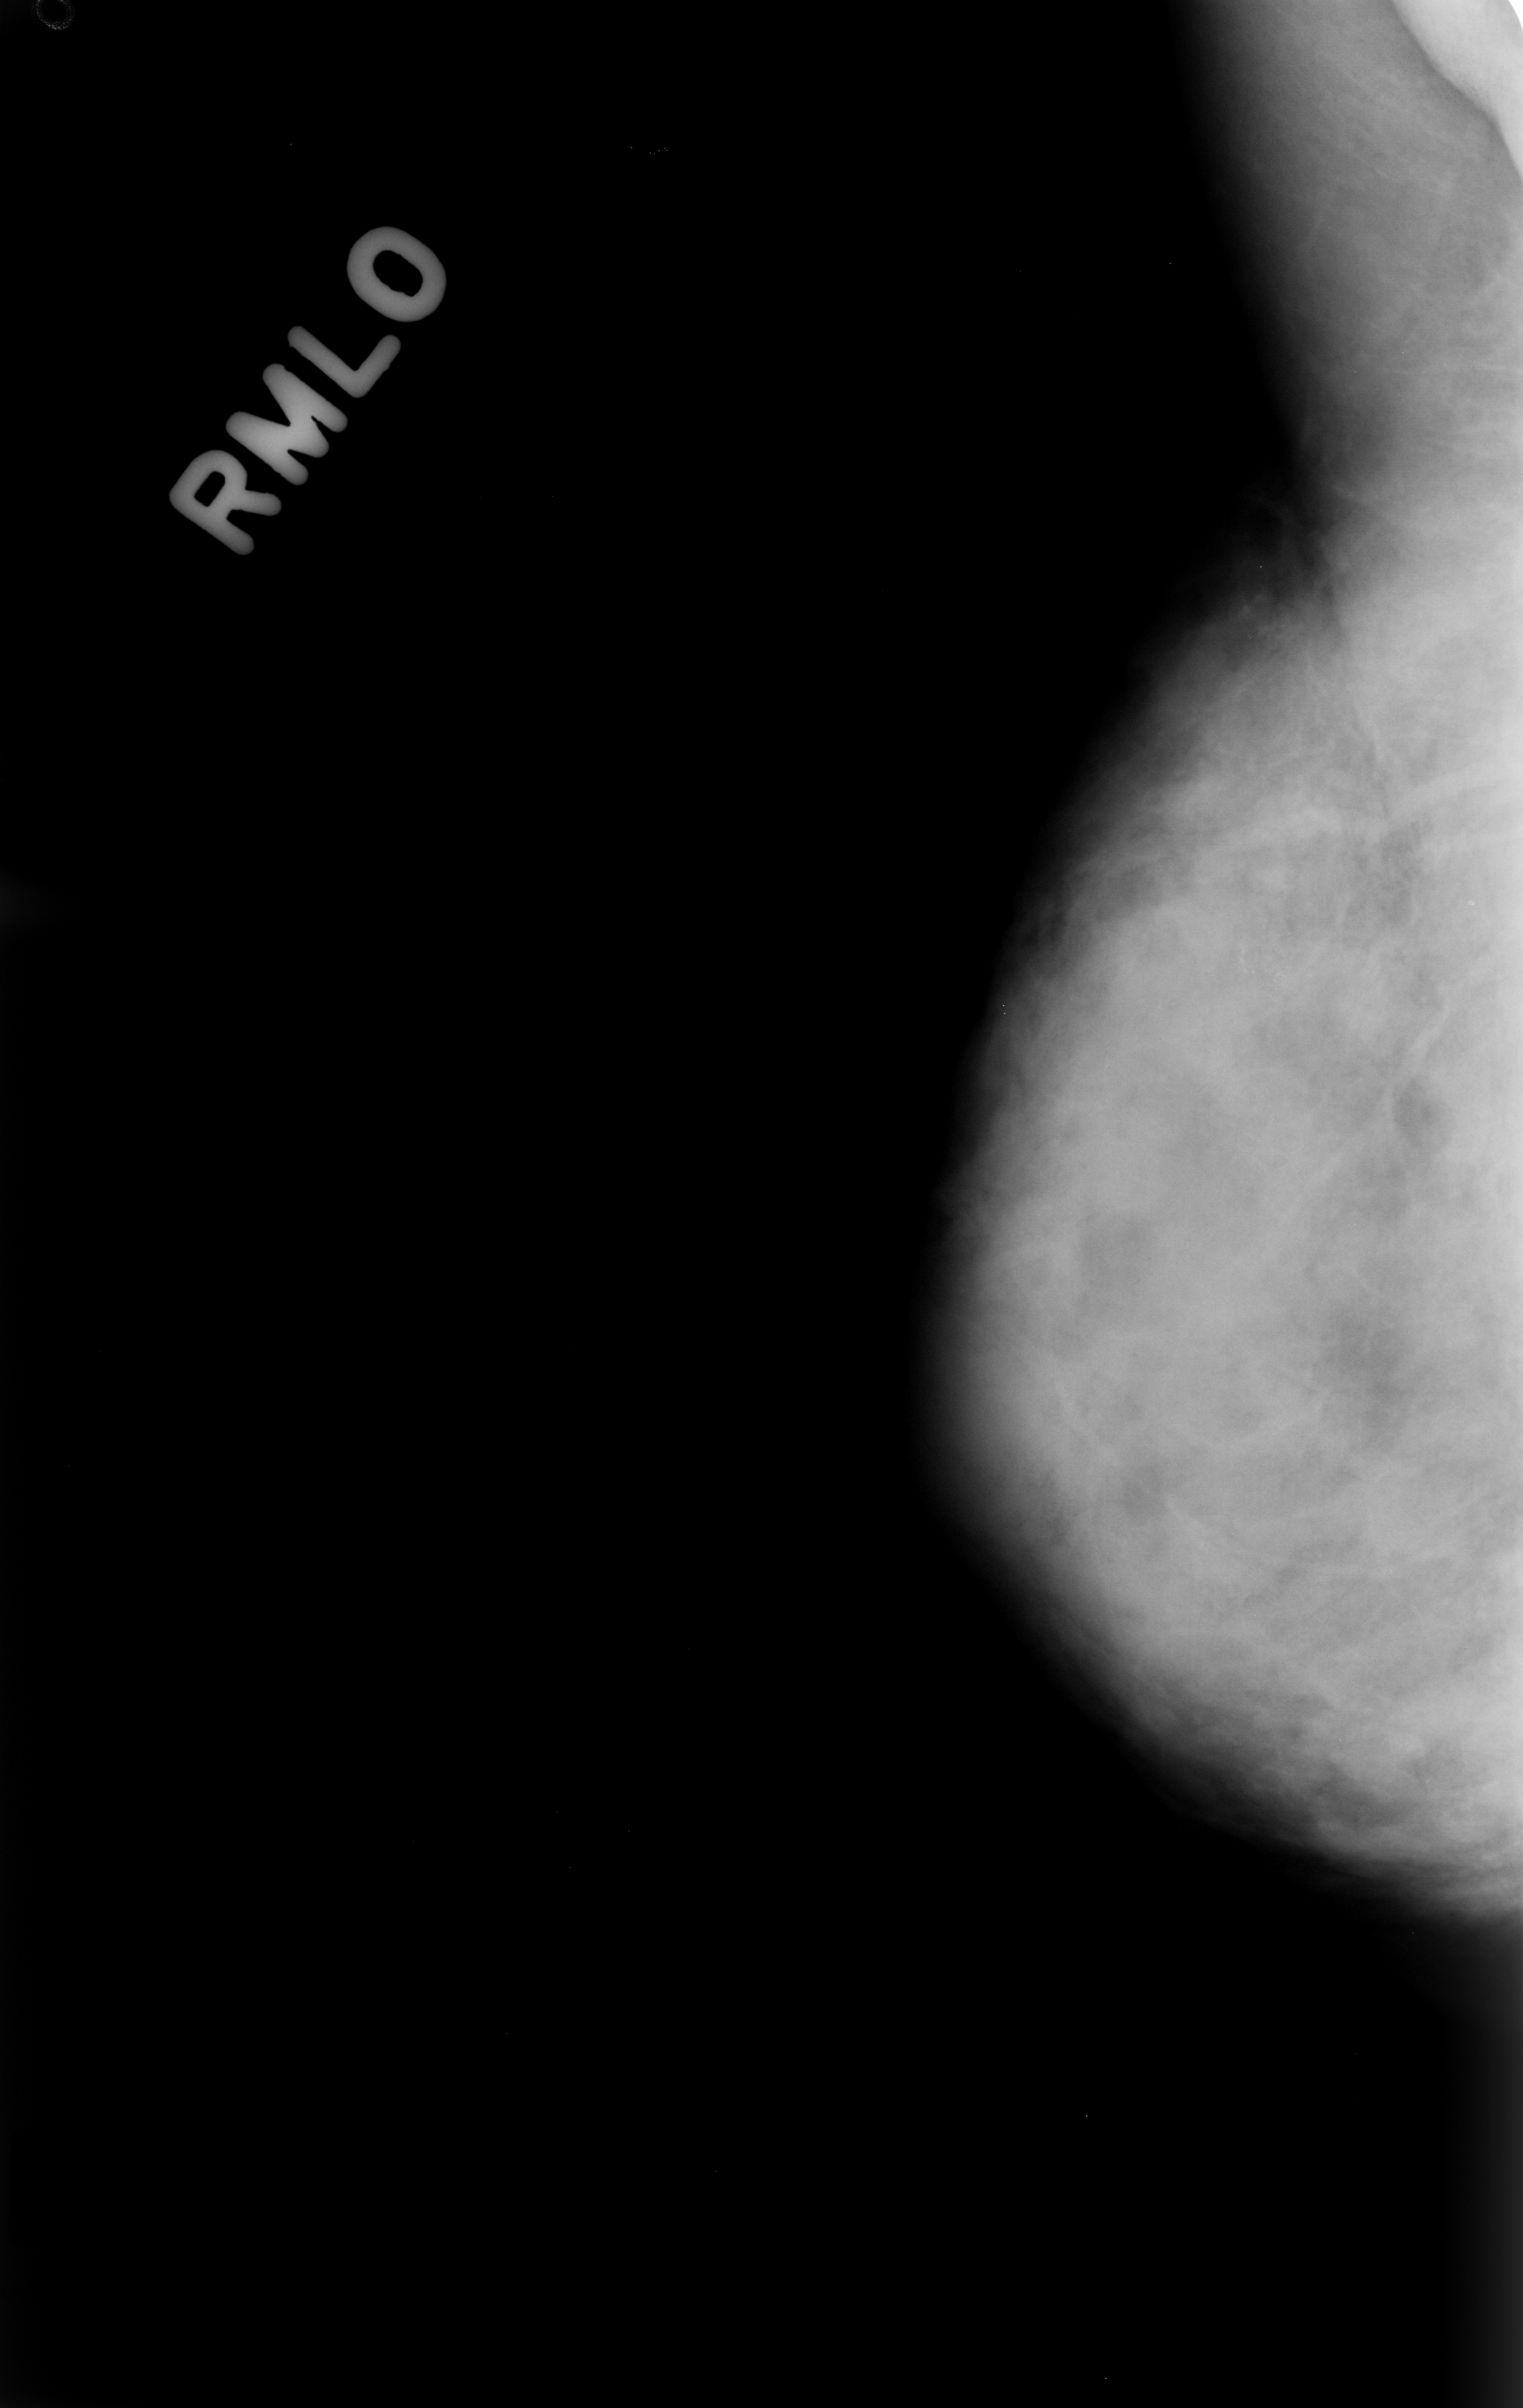
Scanned film-screen mammogram, right breast, mediolateral oblique (MLO) view, breast composition: extremely dense (BI-RADS density category 4 of 4).
- Marked abnormality: calcifications, morphology amorphous, distribution clustered; BI-RADS assessment category 4; subtlety rating 2 on a 1 (subtle) to 5 (obvious) scale; pathology result (as recorded, not read from the image): benign.